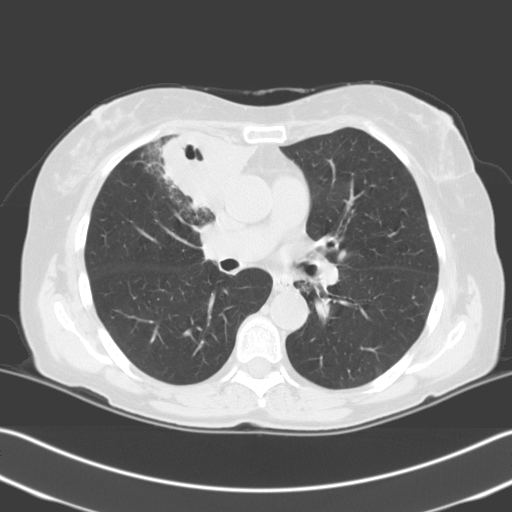
Low-dose screening chest CT, one axial slice. Slice 125 of 204 in the series (ordered by position). 140 kVp. Lung window (W 1500 / L -600 HU). 512 × 512 image matrix.
Annotated regions visible in this slice (manually delineated by an expert):
- lesion 1 (tumor, upper lobe of right lung): box from (x=159, y=132) to (x=256, y=210) px